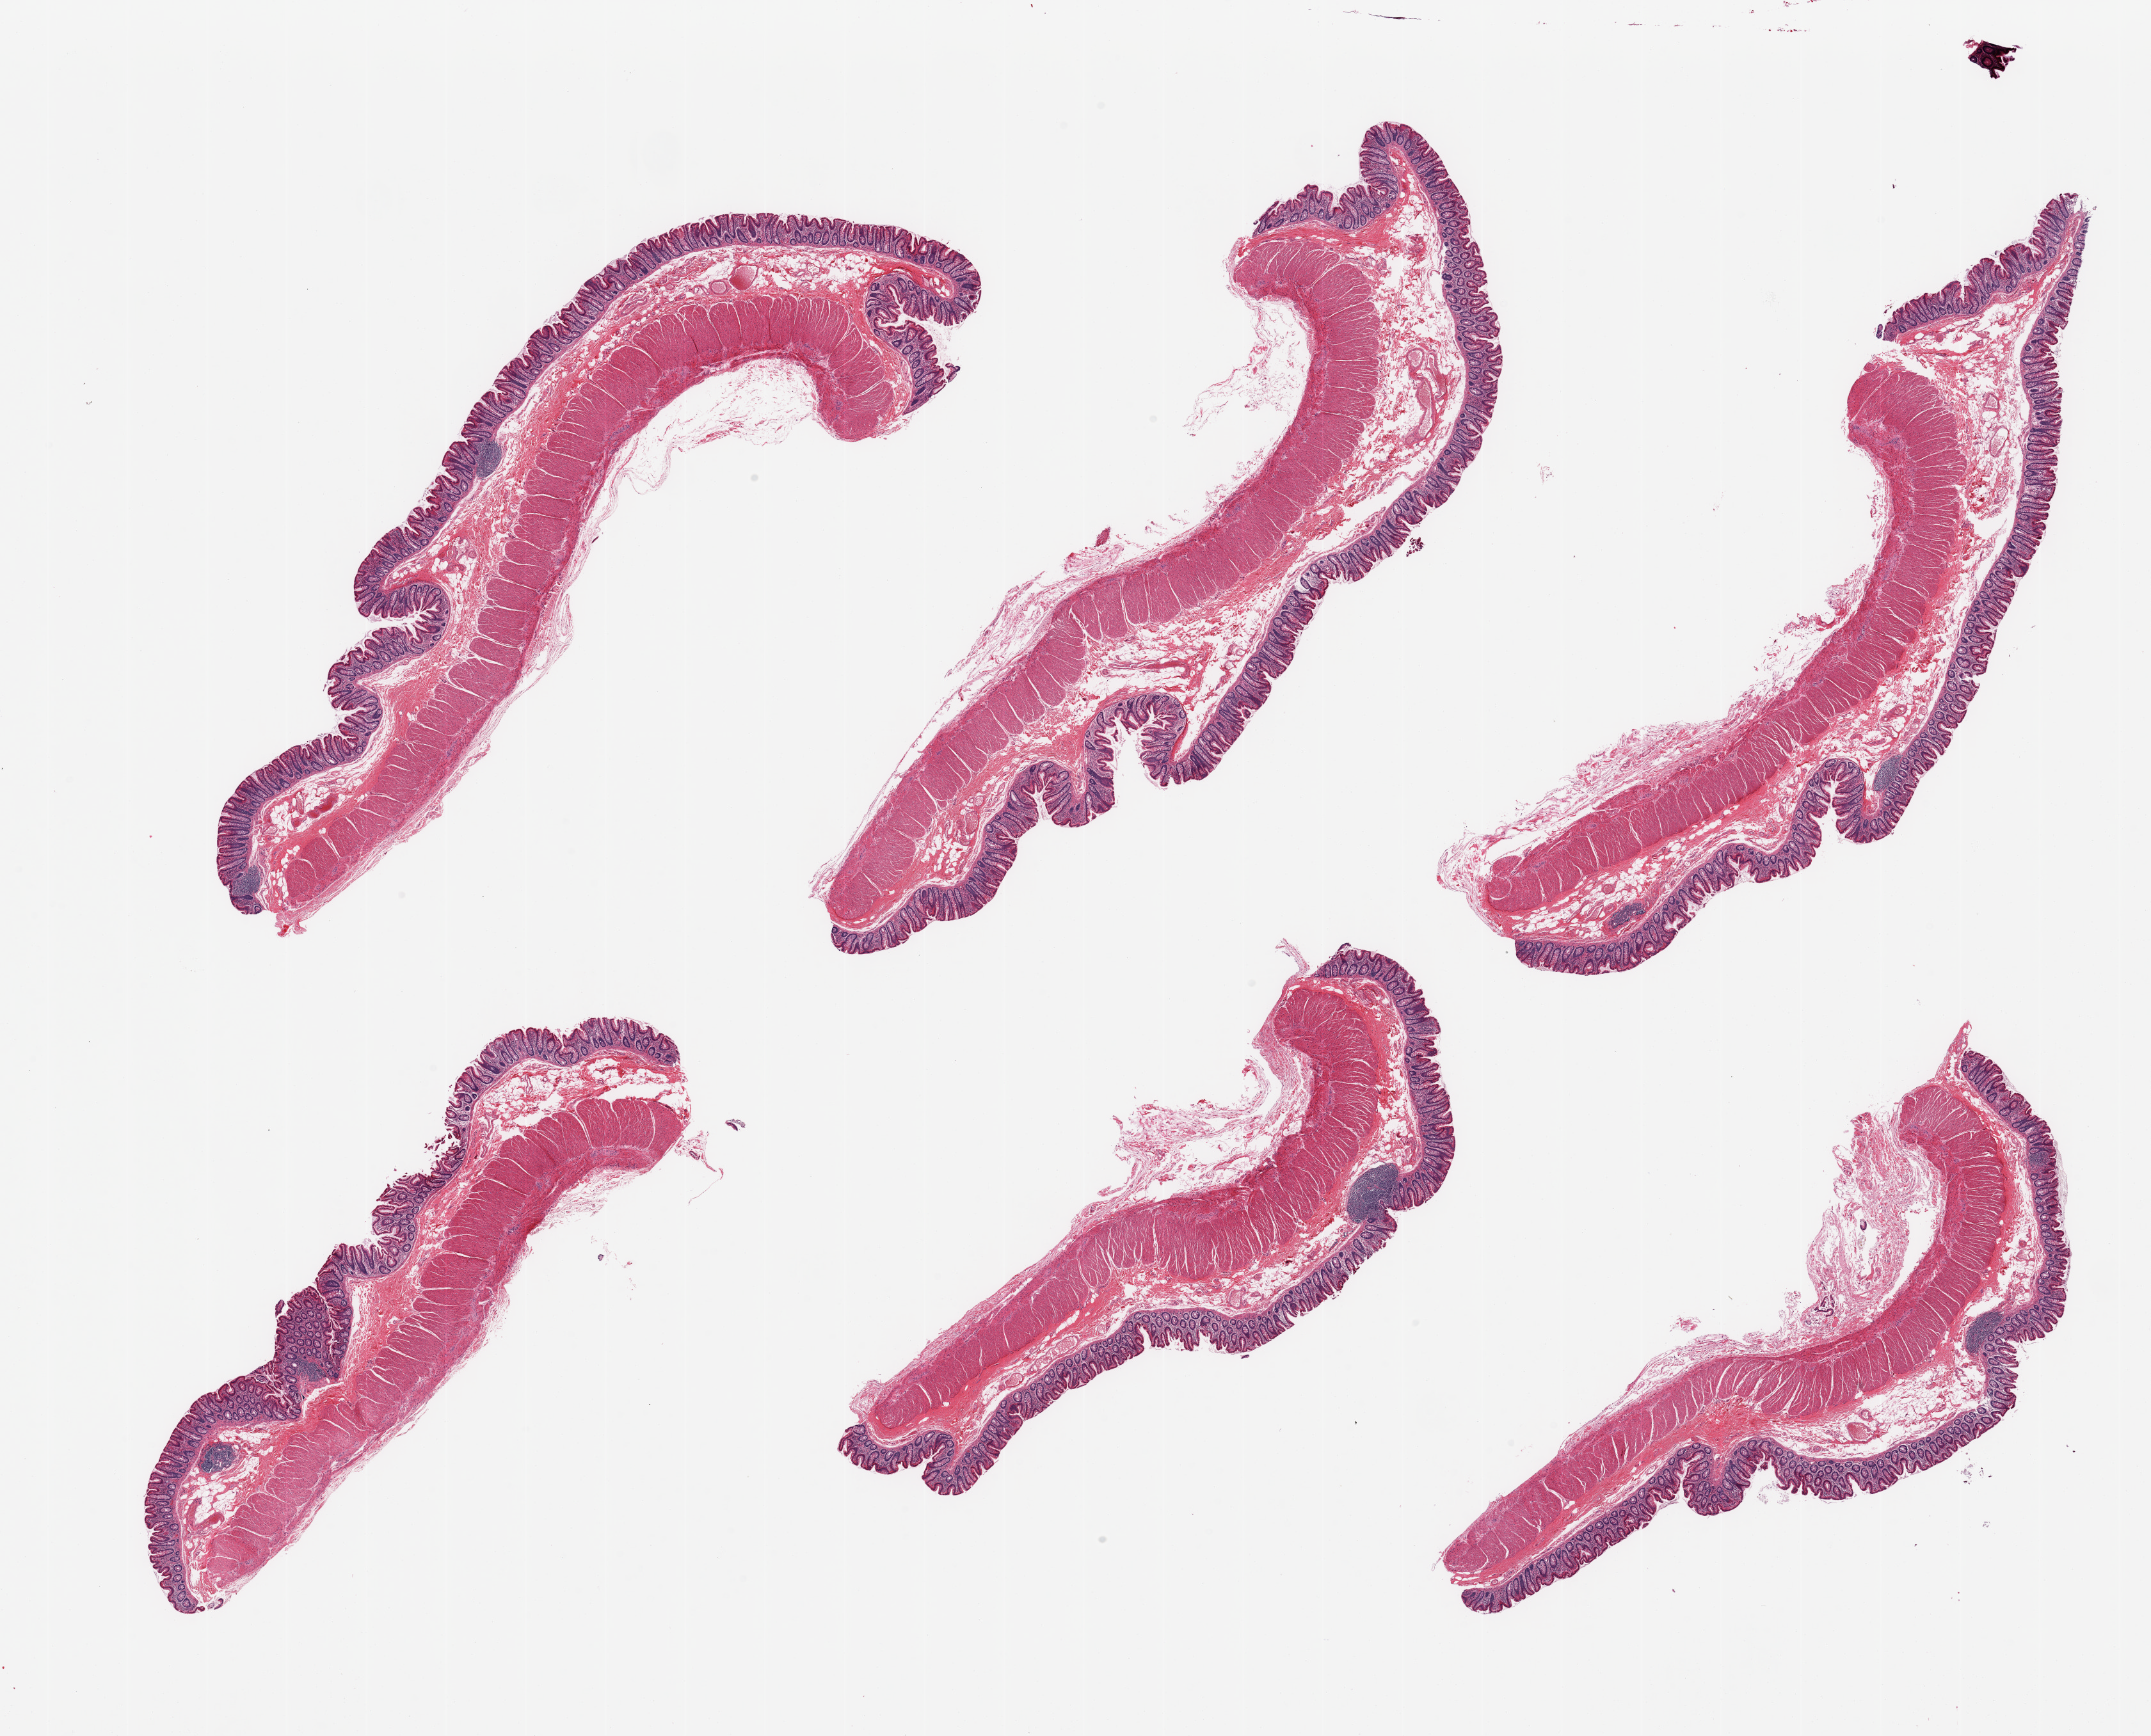
Whole-slide image, hematoxylin and eosin (H&E) stain — a low-resolution overview of the entire scanned area, about 26.6 x 21.5 mm, PAXgene-fixed paraffin-embedded (PFPE) section, target tissue: transverse colon, donor tissue sample. Male donor.
Reviewer comment on this tissue sample: 6 pieces; full thickness sections.